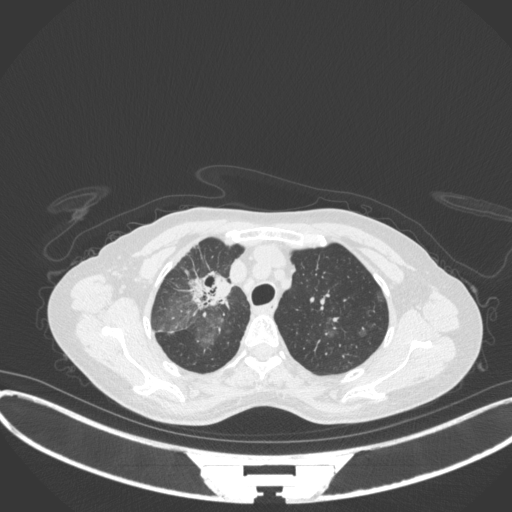
Chest CT, one axial slice; slice 252 of 311 in the series (ordered by position); reconstruction kernel B31f; 120 kVp; lung window (W 1500 / L -600 HU); 1 mm slice thickness; 512 × 512 image matrix. Patient: female, 59 years. Case-level facts recorded for this patient, not image findings: clinical TNM (as recorded): T3 N0 M0; histopathological grade: G1.
Structures marked on this image (bounding box drawn by a radiologist):
- lung tumour (recorded histology: adenocarcinoma): bounding box (x1, y1, x2, y2) in pixels: (186, 268, 235, 315)